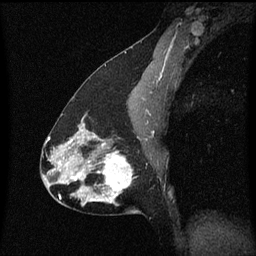
Breast MRI (dynamic contrast-enhanced), one sagittal slice. Slice 32 of 60 in the series (ordered by position). Dynamic contrast-enhanced series, image 2 of 3 at this slice position (ordered by acquisition). 1.5 T. TE 4.2 ms, TR 8.4 ms. 256 × 256 image matrix. Female patient, age 47 years.
Outlined on this slice (semi-automatically segmented with operator editing):
- analysis volume of interest (the breast-tissue region the enhancement analysis was run in; not a lesion): bounding box <81,138,142,213> (left, top, right, bottom; pixels)
- tumour enhancement mask (voxels above the 70 % enhancement threshold inside the analysis volume of interest): <81,138,132,203>